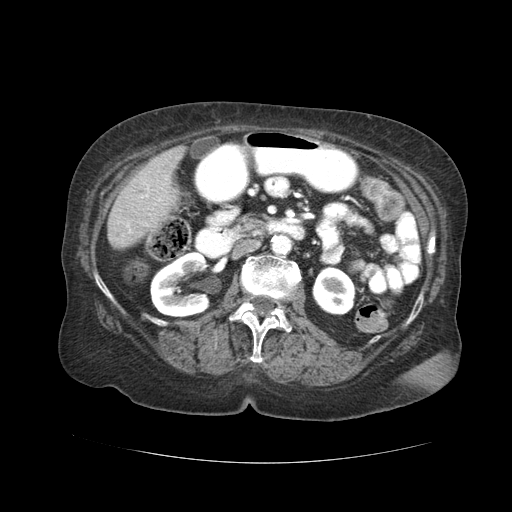
Contrast-enhanced abdominal CT (liver protocol), one axial slice. Slice 3 of 59 in the series (ordered by position). Reconstruction kernel STANDARD. Soft-tissue window (W 400 / L 40 HU). 2.5 mm slice thickness. 512 × 512 image matrix, field of view 380 × 380 mm. Case-level facts recorded for this patient, not image findings: diagnosis: hepatocellular carcinoma (patient treated with transarterial chemoembolisation; whether this scan precedes or follows treatment is not stated here); TNM stage (as recorded): Stage-I.
Outlined on this slice (semi-automatically segmented with operator editing):
- liver parenchyma outside the tumour (the mass and vessels are separate outlines, so this box may not span the whole liver): bounding box [x1, y1, x2, y2] px = [108, 146, 184, 248]